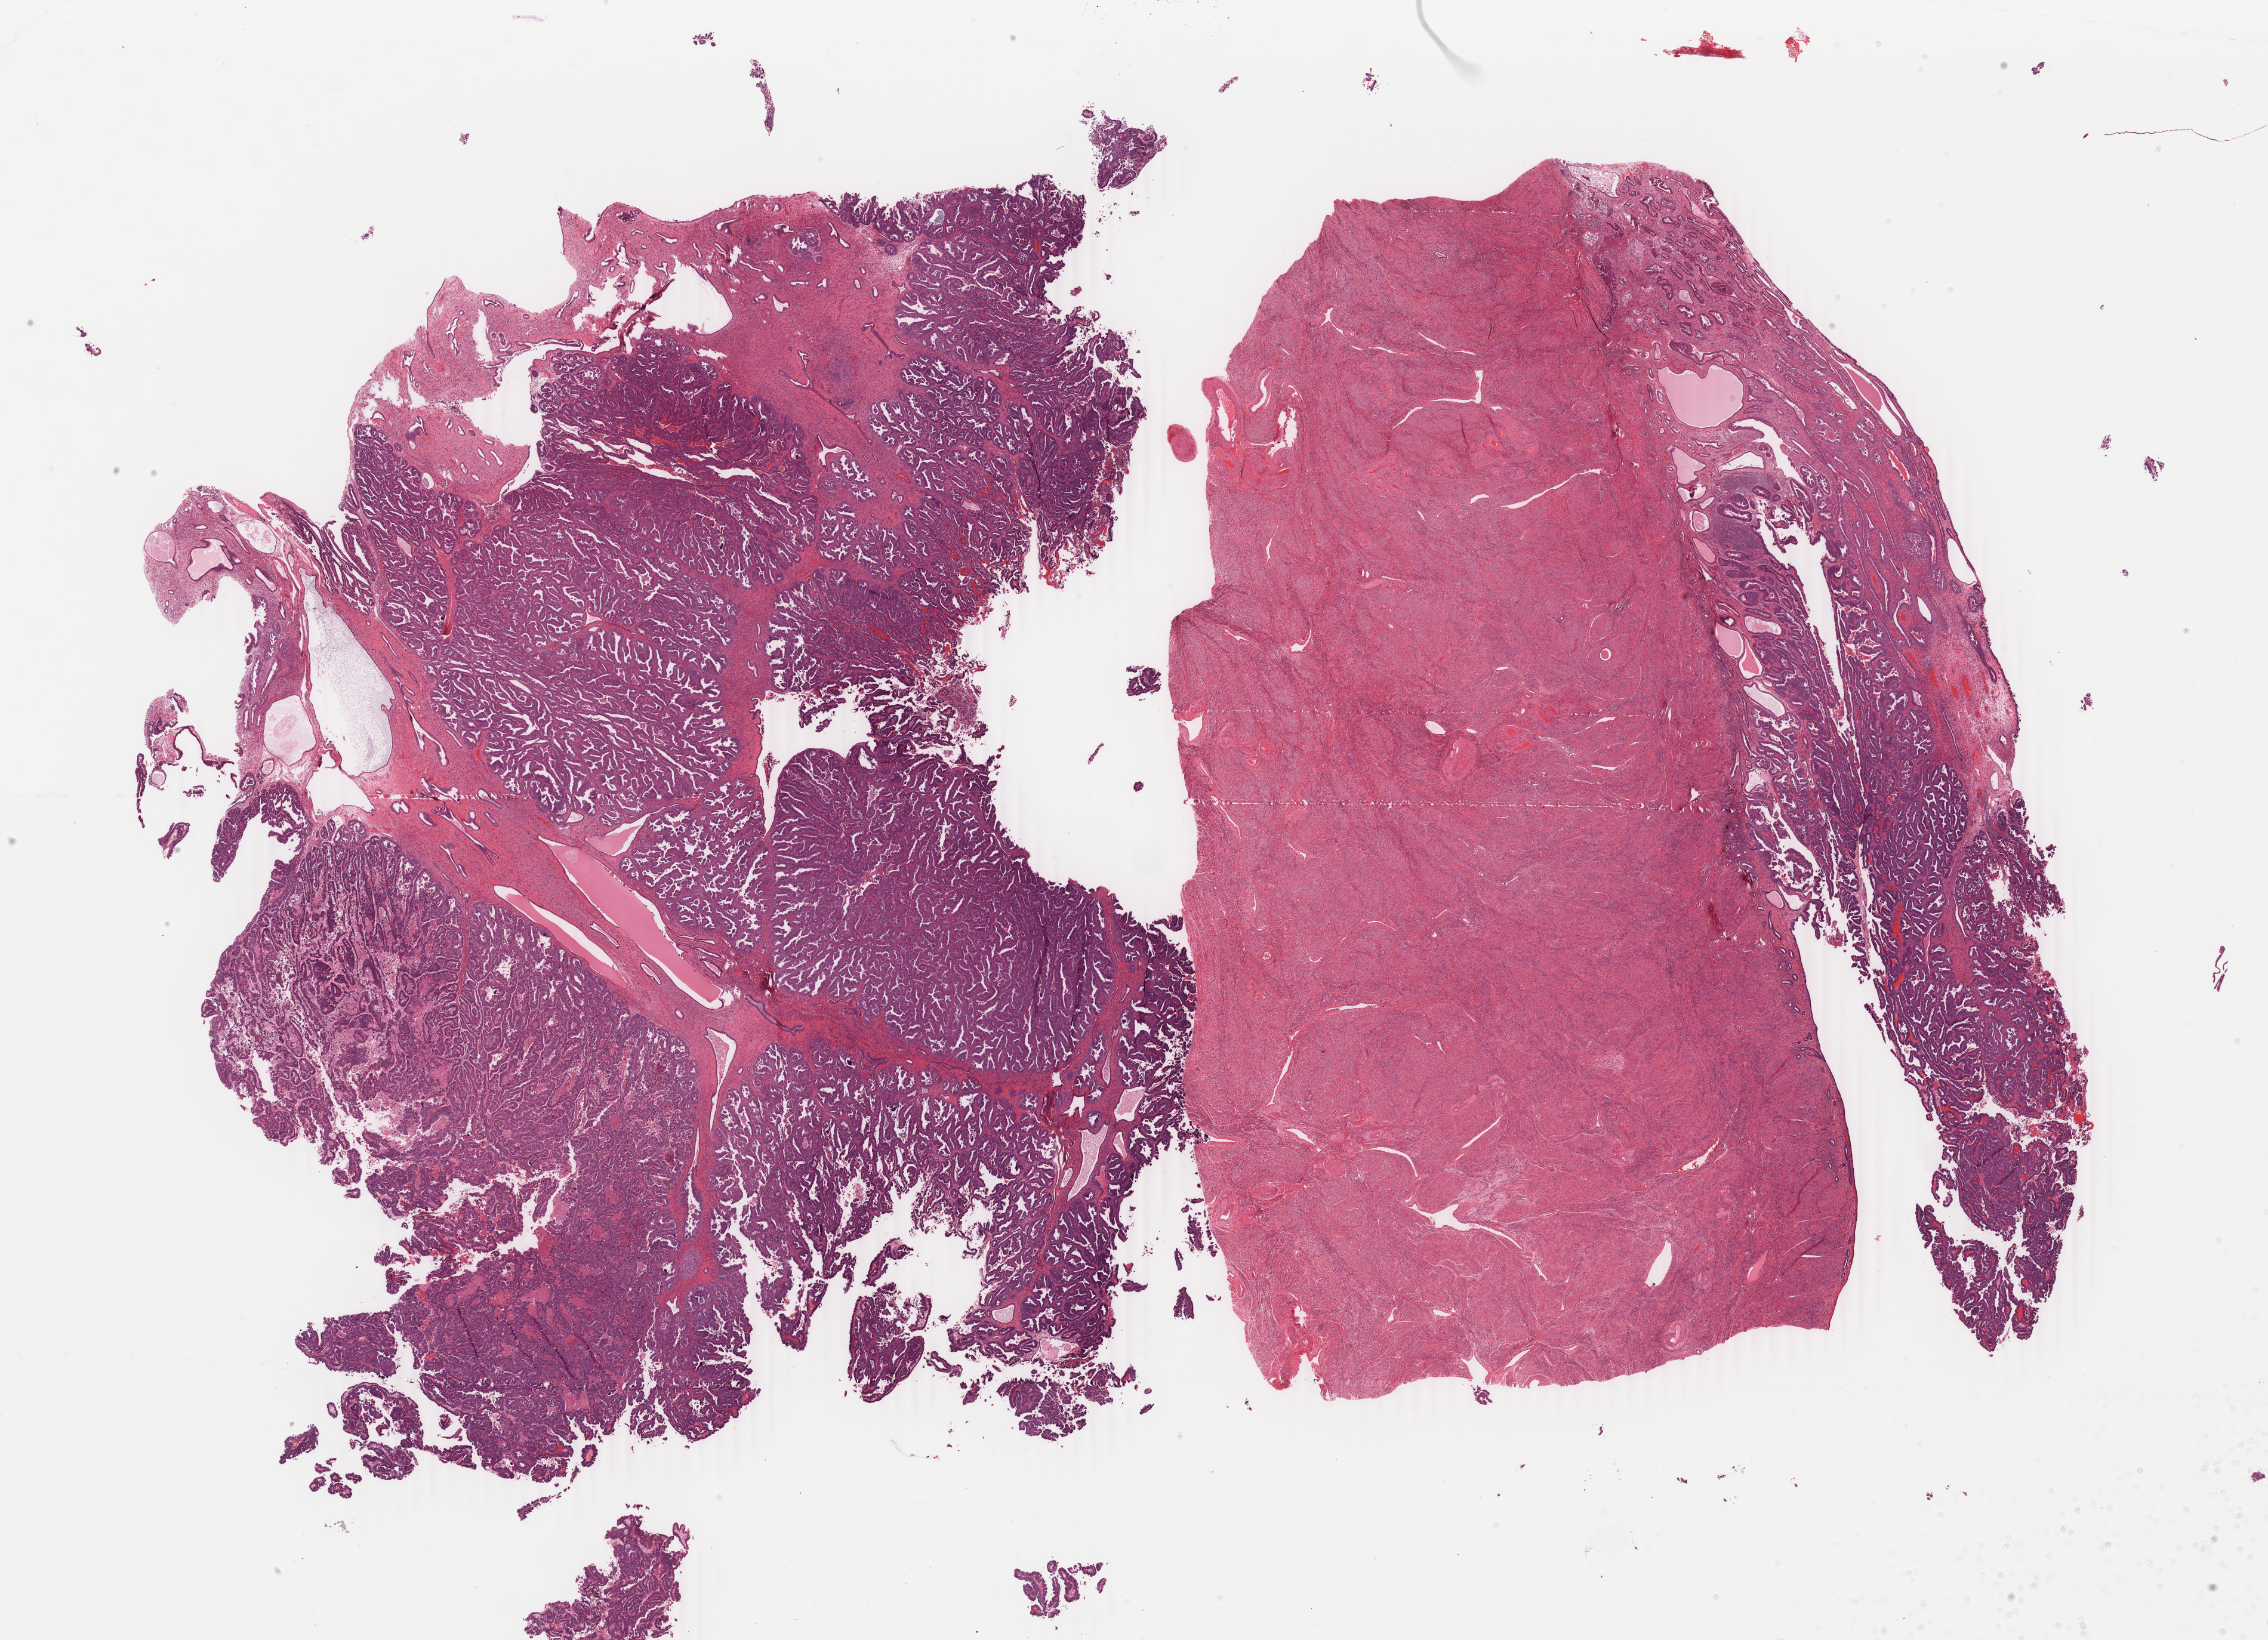
H&E whole-slide image, whole scanned area (about 30.2 x 21.9 mm) shown as a low-resolution overview, formalin-fixed paraffin-embedded (FFPE) diagnostic section, primary tumour sample from the uterus. Female, age 68 years at initial diagnosis. Histologic grade: high grade.
Lymph nodes positive (case pathology): 0 of 10 examined. Diagnosis: Serous cystadenocarcinoma, NOS (endometrium). FIGO stage: IA.